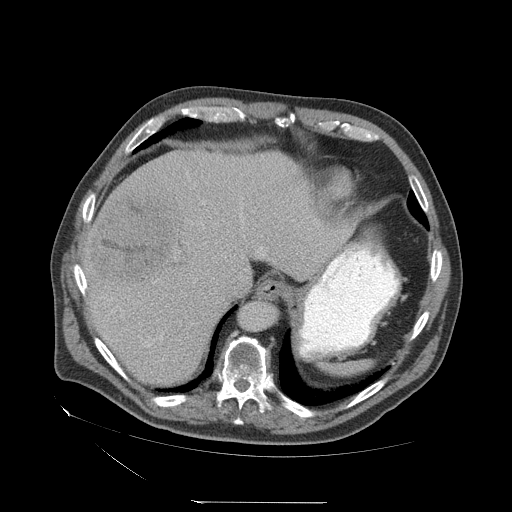
Contrast-enhanced abdominal CT (liver protocol), one axial slice. Slice 53 of 83 in the series (ordered by position). Reconstruction kernel STANDARD. Soft-tissue window (W 400 / L 40 HU). 2.5 mm slice thickness. 512 × 512 image matrix, field of view 460 × 460 mm. From the clinical record (not read from this slice): diagnosis: hepatocellular carcinoma (patient treated with transarterial chemoembolisation; whether this scan precedes or follows treatment is not stated here); TNM stage (as recorded): Stage-I; Child-Pugh class: A; tumour differentiation: well differentiated; tumour nodularity: uninodular.
Structures marked on this image (semi-automatic segmentation, software-assisted and operator-edited):
- liver parenchyma outside the tumour (the mass and vessels are separate outlines, so this box may not span the whole liver): bounding box <82,148,352,386> (left, top, right, bottom; pixels)
- mass: <87,194,179,291>
- liver vessels: <148,282,155,346>